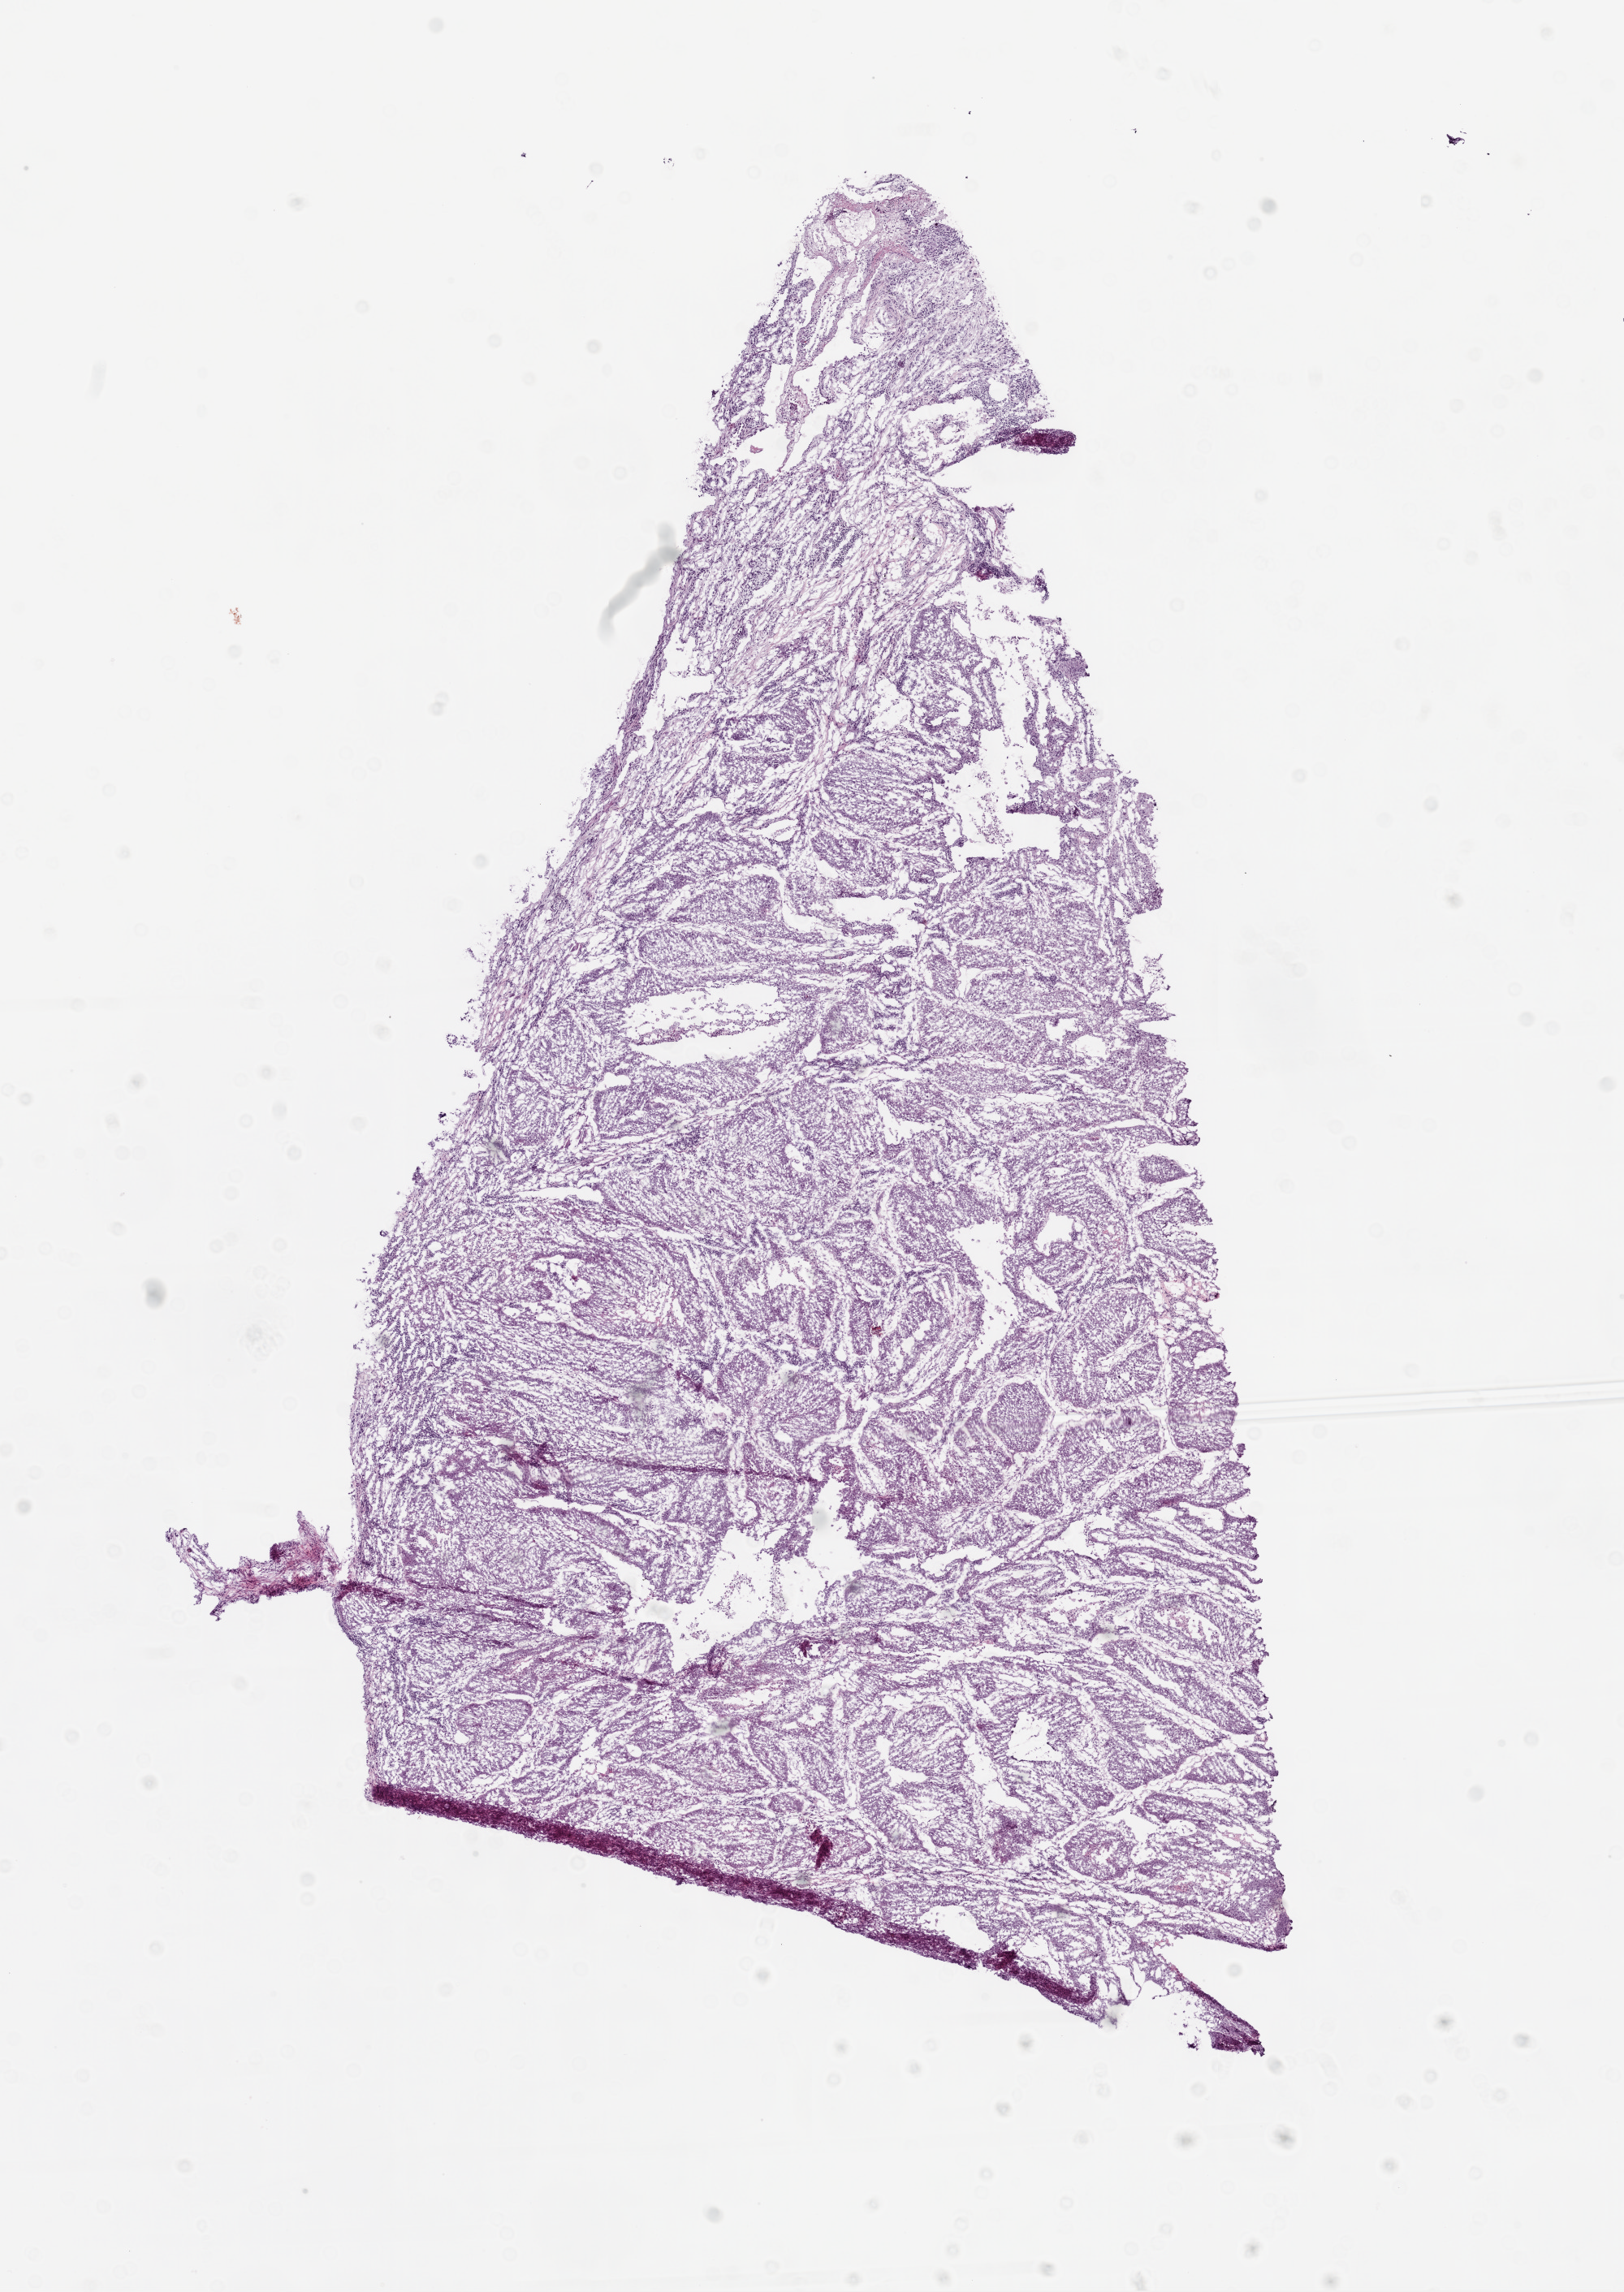
Digitized Hematoxylin and eosin (H&E) stained tissue section (whole slide) — low-resolution overview of the scanned area, about 8.0 x 11.3 mm. Frozen section. Sample: primary tumour, lung. Patient: female, age at initial diagnosis 76 years. Composition of this section per pathologist review: tumour cells 85%, tumour nuclei 80%, normal cells 0%, stromal cells 10%, necrosis 5%.
* TNM: T2 N0 M0
* AJCC pathologic stage: IIA
* pathologic diagnosis: Squamous cell carcinoma, NOS (upper lobe, lung)